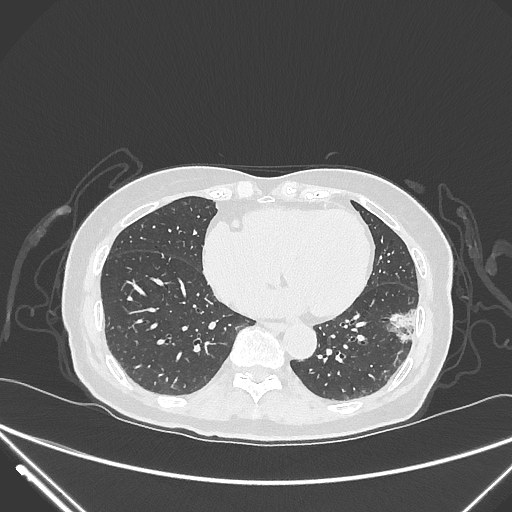
Chest CT, one axial slice; slice 110 of 310 in the series (ordered by position); reconstruction kernel IMR1,SharpPlus; 120 kVp; lung window (W 1500 / L -600 HU); 1 mm slice thickness; 512 × 512 image matrix. Female patient, age 82 years. Case-level facts recorded for this patient, not image findings: clinical TNM (as recorded): T1c N0 M0; histopathological grade: G2.
Annotated regions visible in this slice (bounding box drawn by a radiologist):
- lung tumour (recorded histology: adenocarcinoma): bounding box [x1, y1, x2, y2] px = [386, 303, 421, 347]